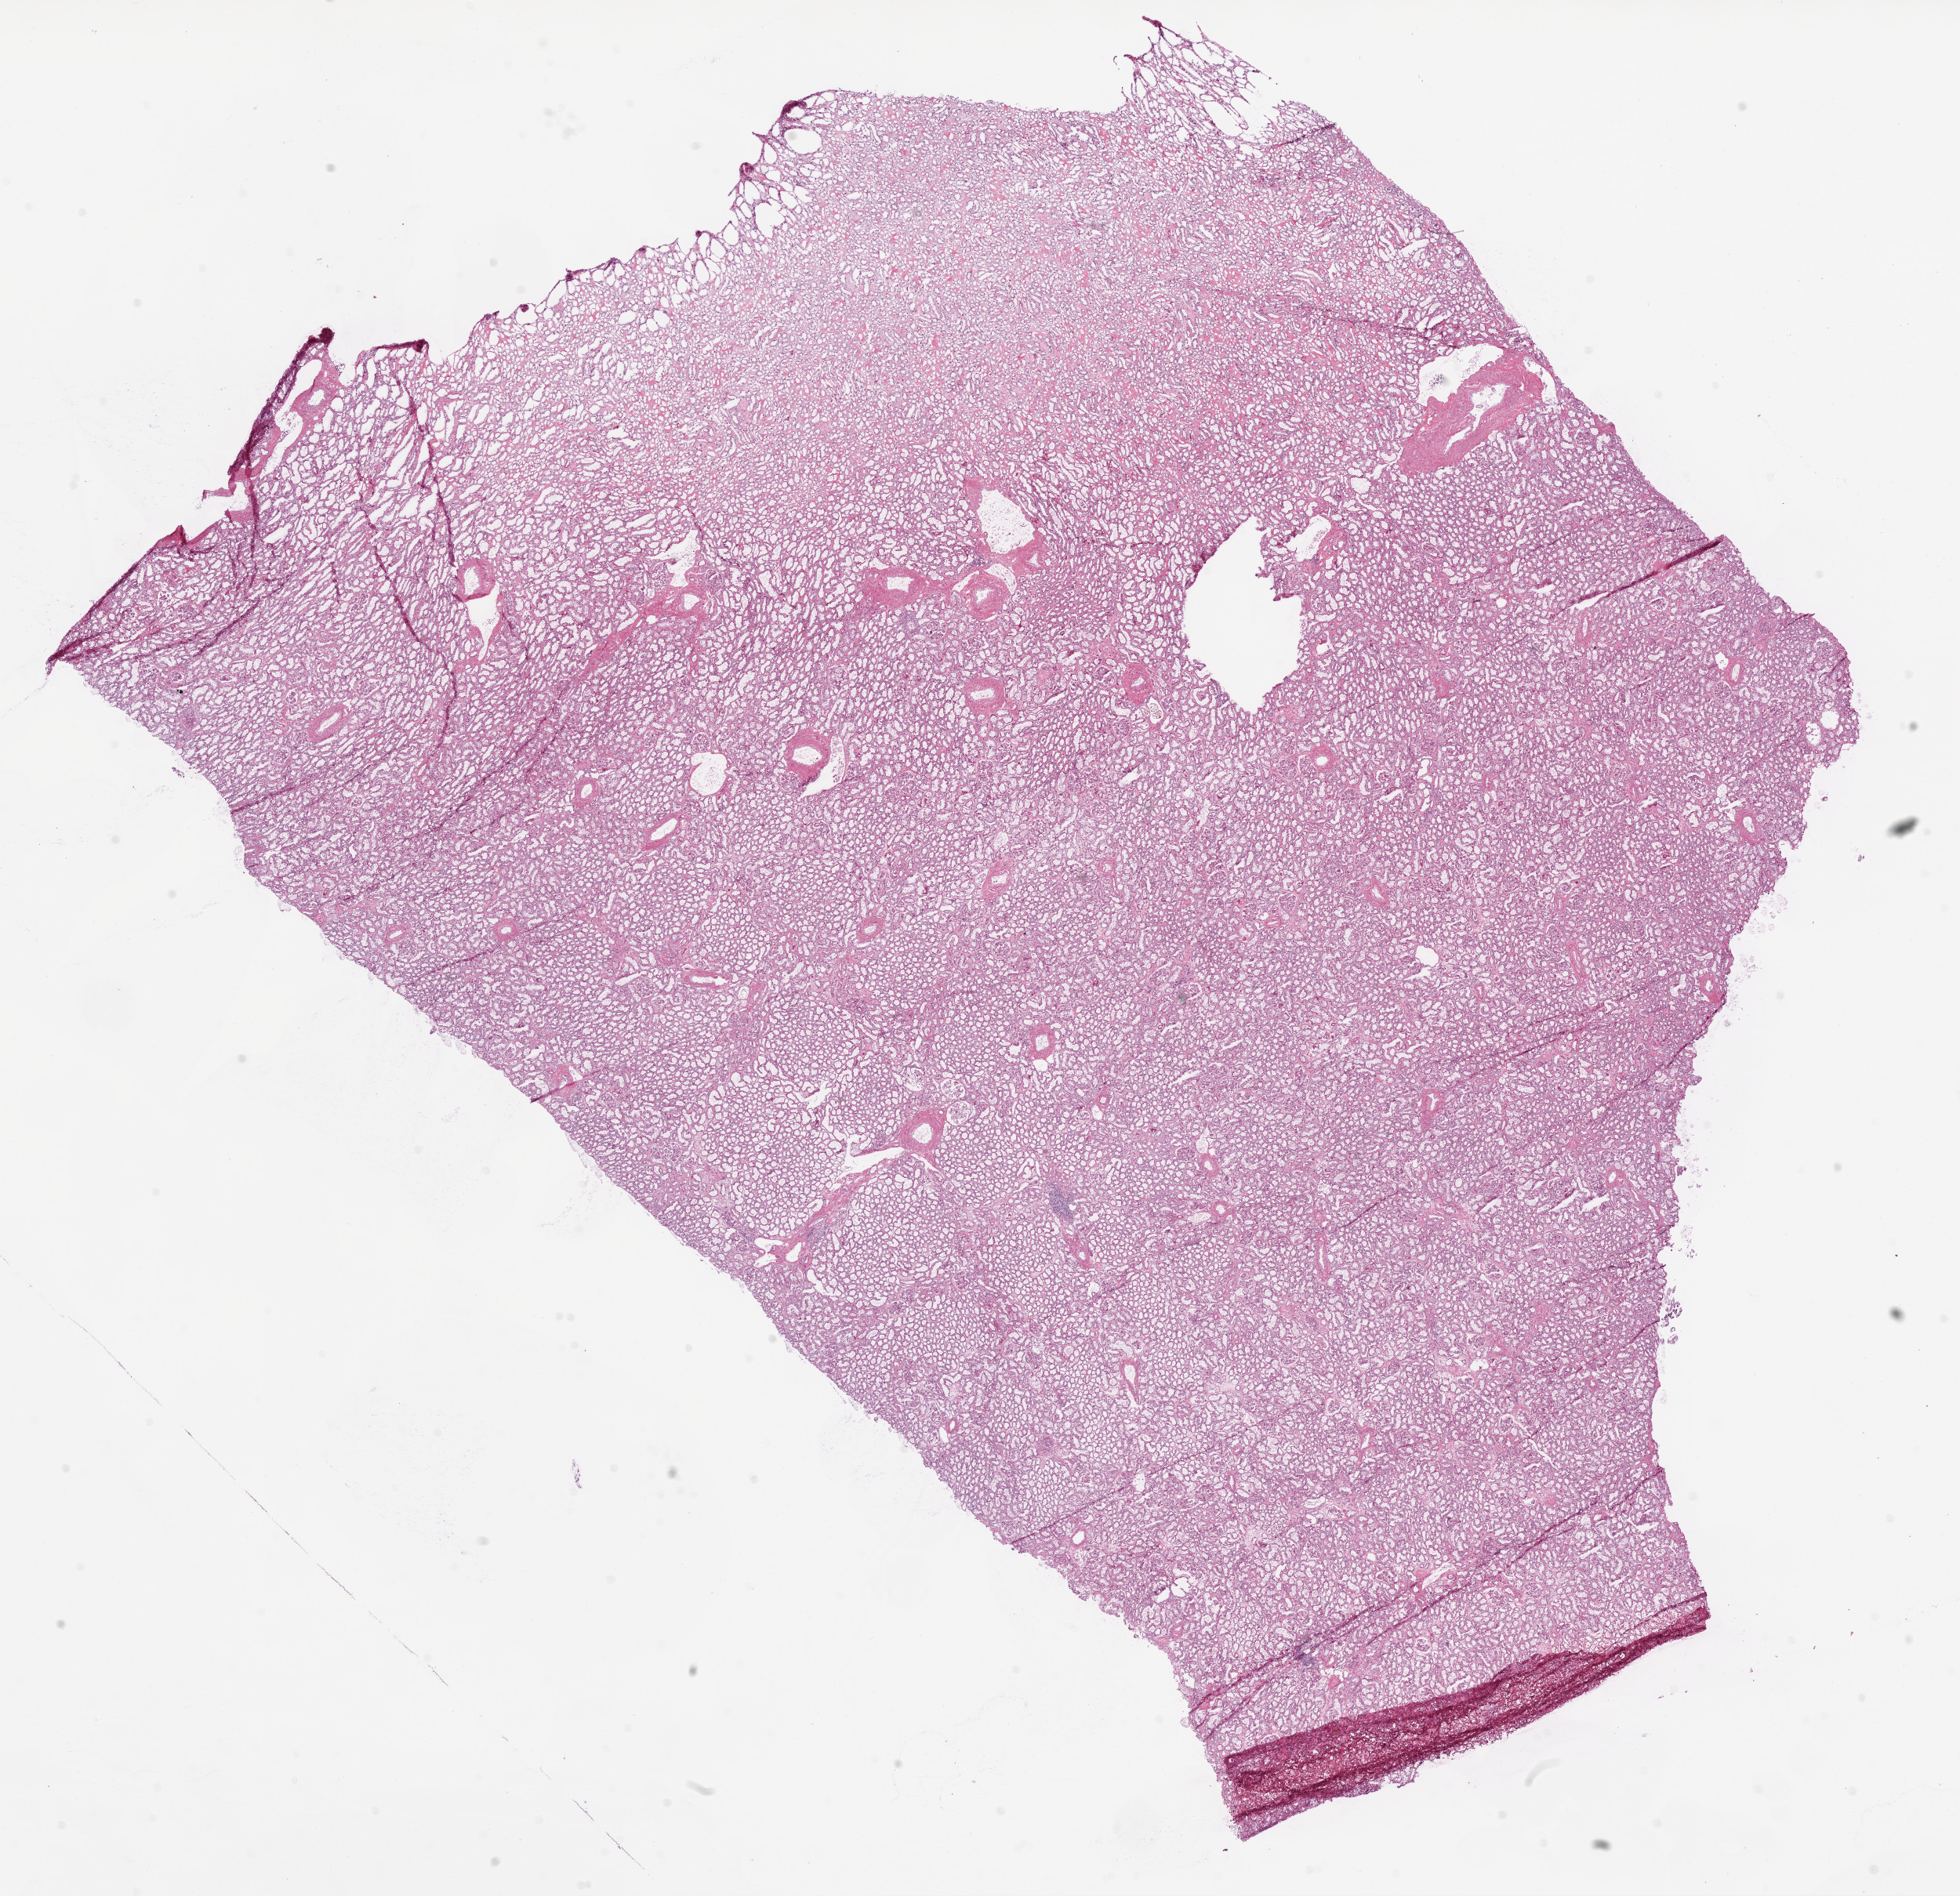
Hematoxylin and eosin (H&E) stained whole-slide image — shown as a low-resolution overview of the whole scanned area (about 20.1 x 19.4 mm). Frozen section from the bottom of the tissue portion. Solid tissue normal (non-tumour tissue) sample from the kidney. Male, age 74 years at initial diagnosis.
This section: solid tissue normal sample (biorepository sample class). Patient diagnosis: Clear cell adenocarcinoma, NOS.